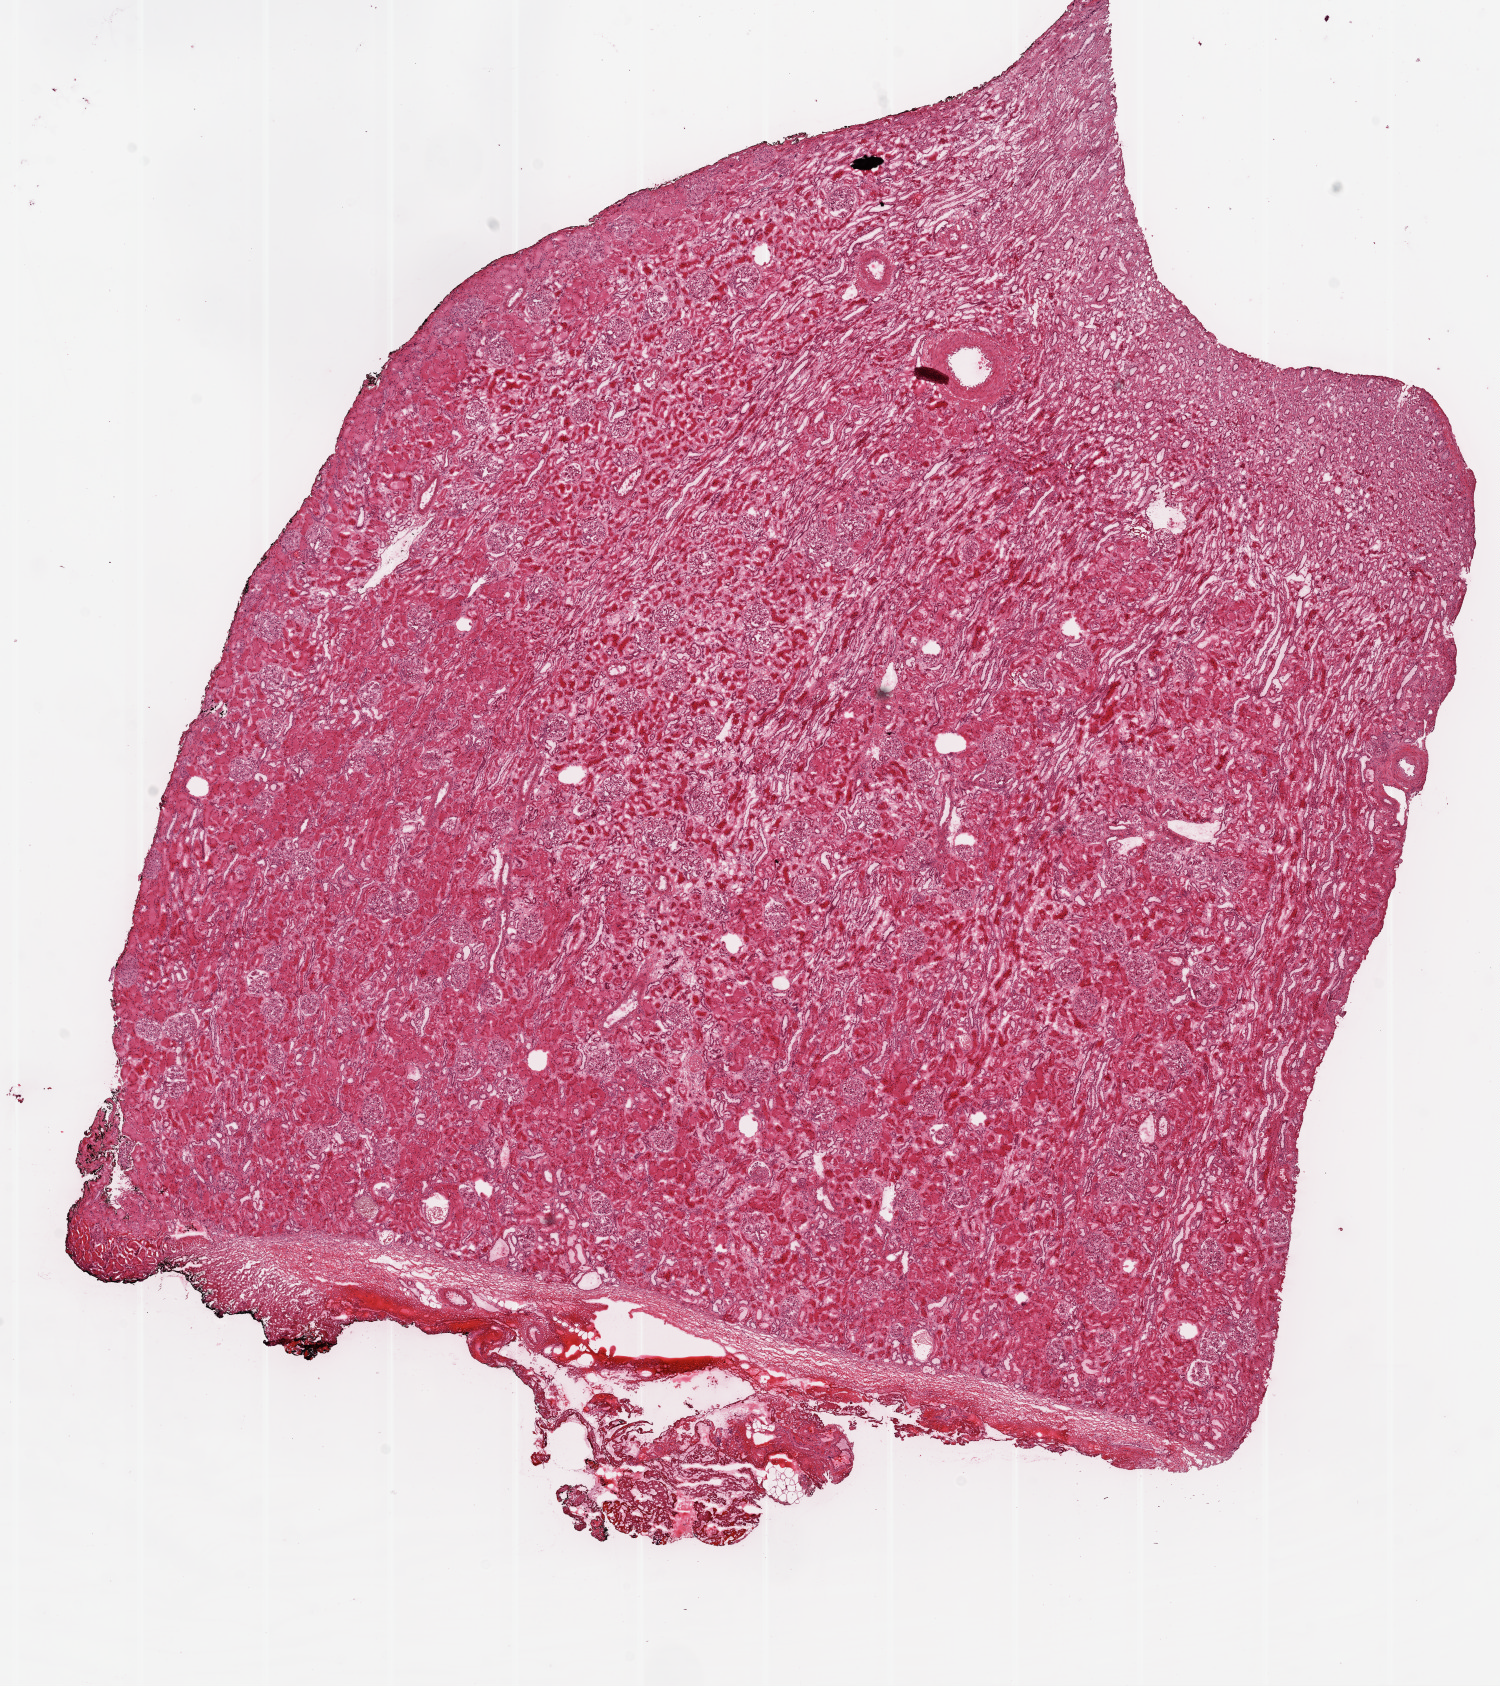
Digitized H&E-stained tissue section (whole slide), a low-resolution overview of the entire scanned area, about 12.0 x 13.5 mm. Frozen section from the top of the tissue portion. Solid tissue normal (non-tumour tissue) sample from the kidney. Male patient; age at initial diagnosis 39 years.
This section: solid tissue normal (non-tumour) sample from the same patient. Patient diagnosis: Clear cell adenocarcinoma, NOS.